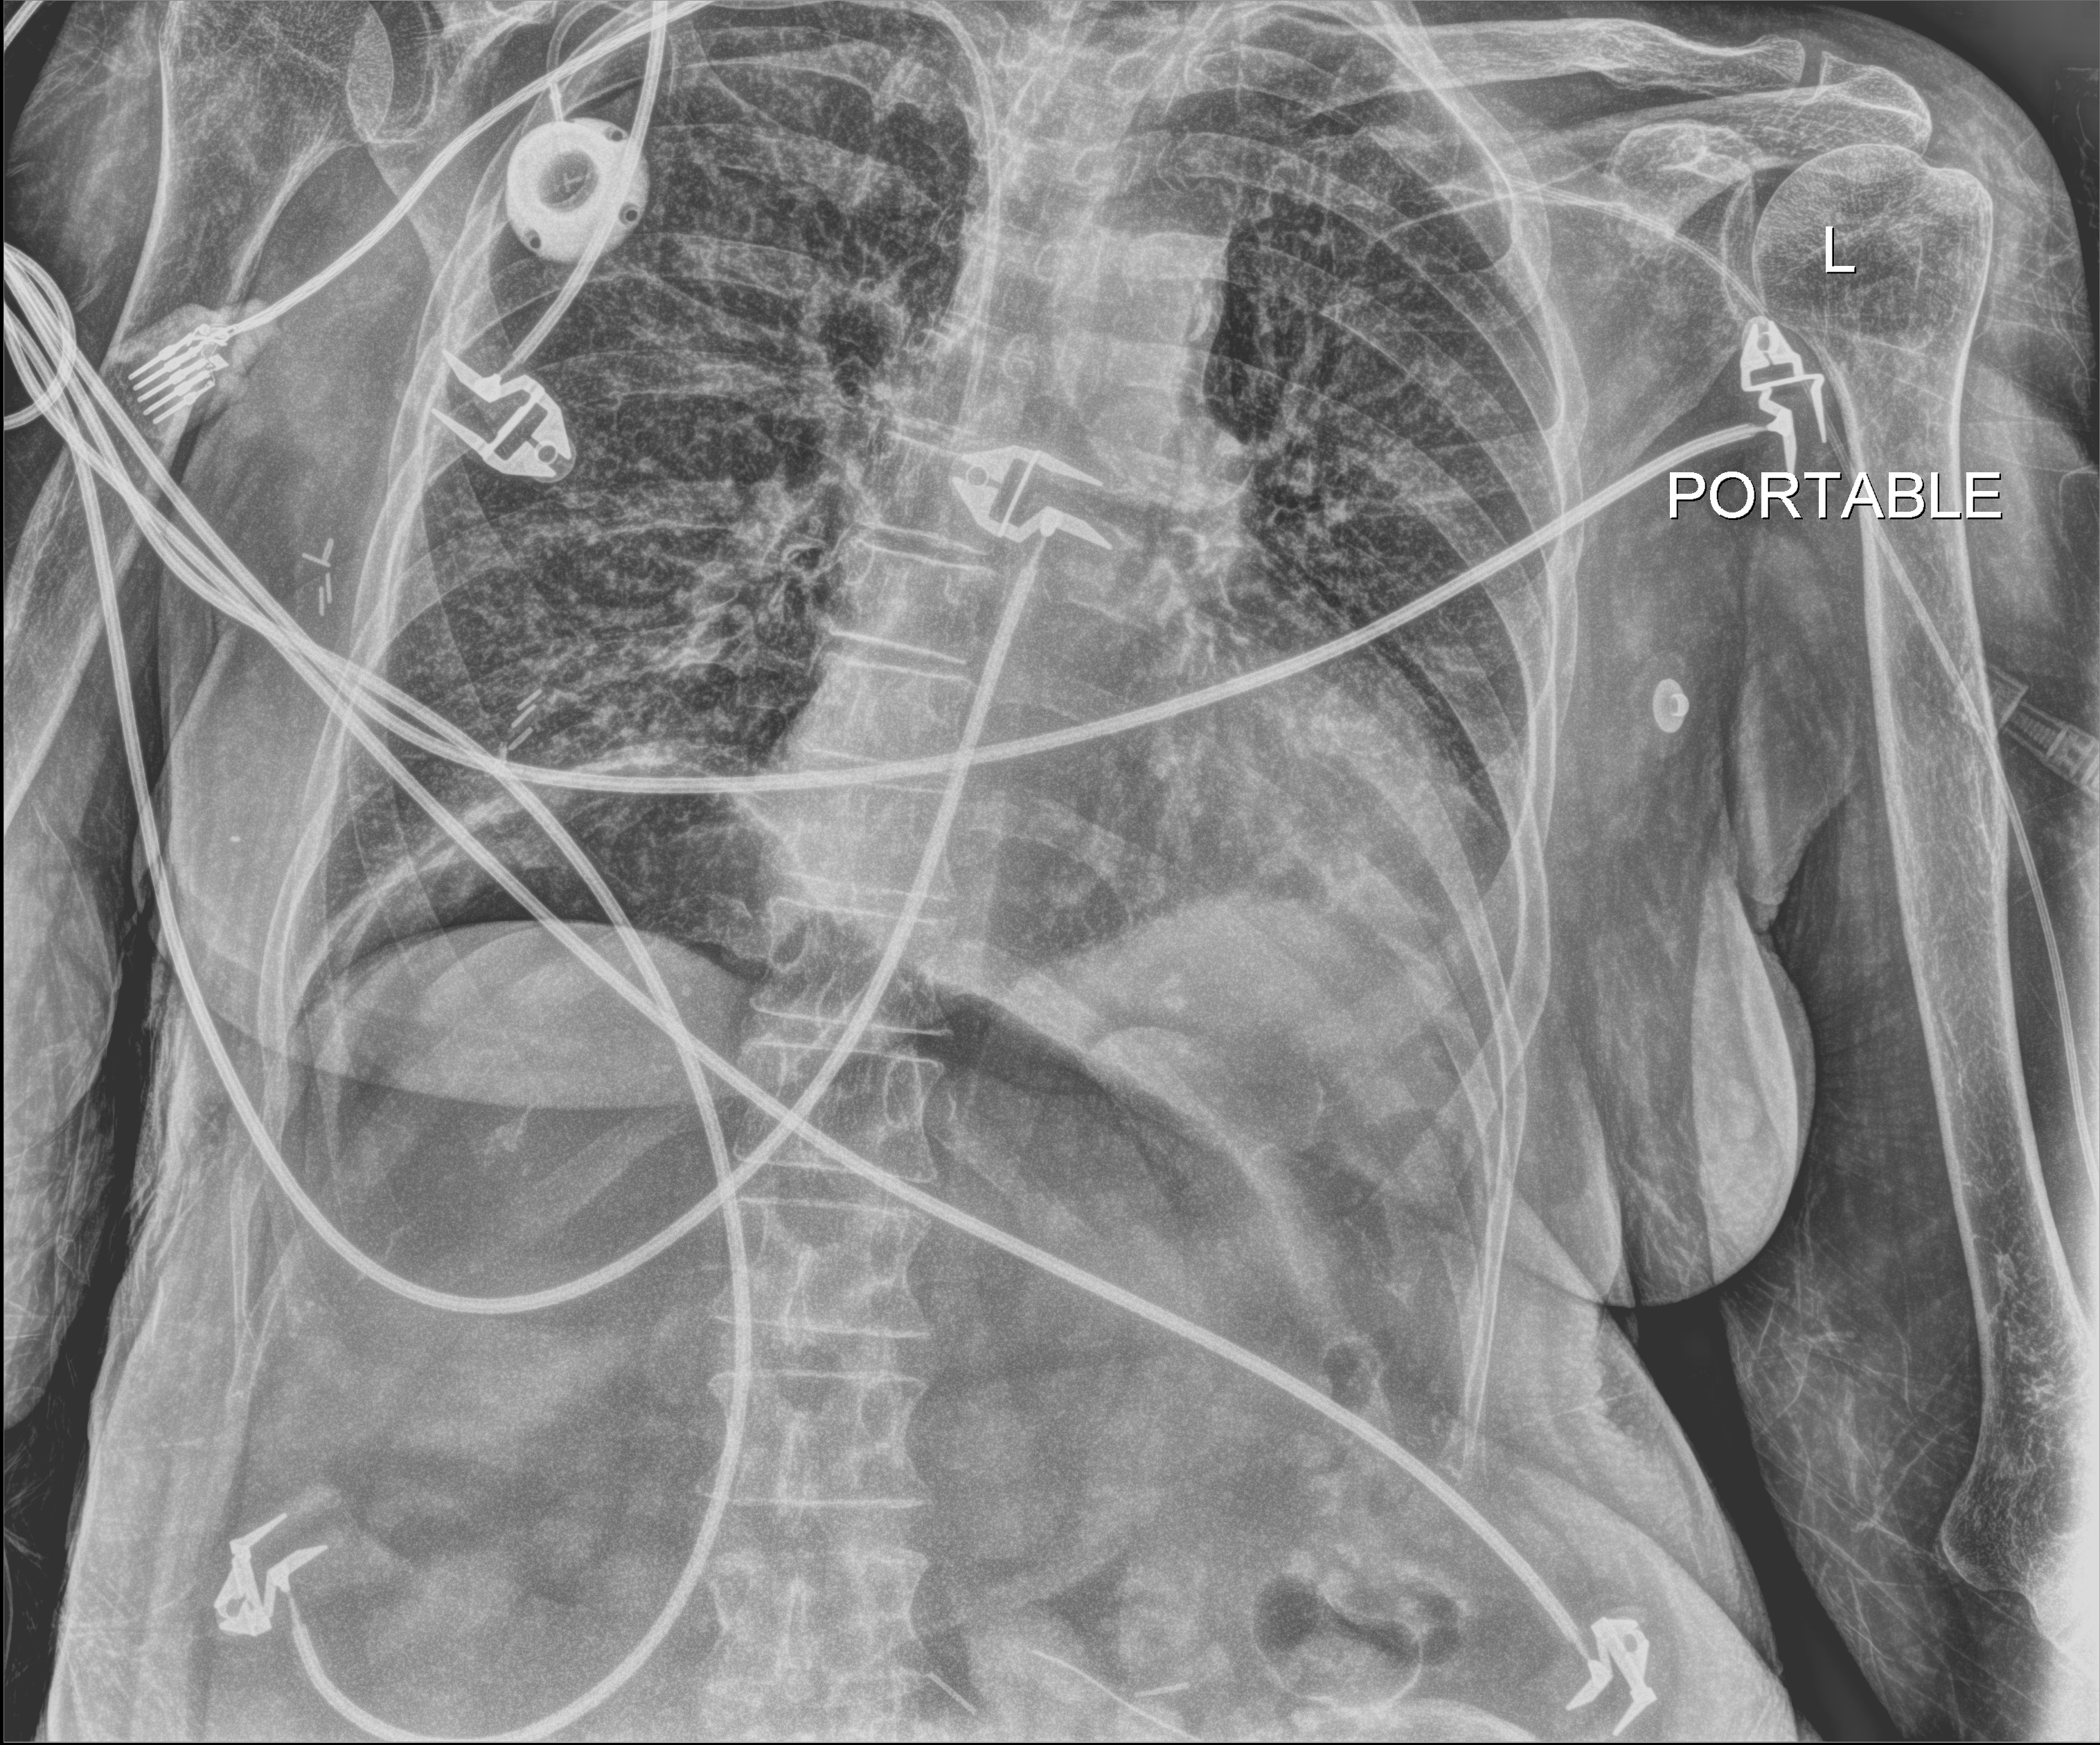
Portable chest radiograph. Female patient hospitalised with COVID-19, age 60–74 years.
Hospital-stay facts (about this admission, not read from this image; timing relative to this image not recorded):
- mechanically ventilated during this hospital stay: yes
- chronic kidney disease (admission record): no
- admitted to intensive care during this hospital stay: yes